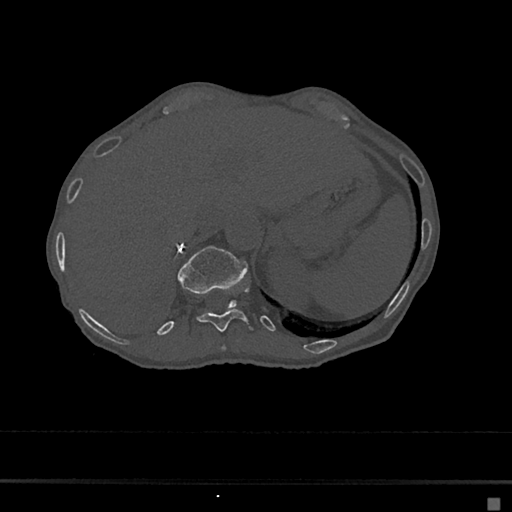
CT including the spine, one axial slice; slice 161 of 797 in the series (ordered by position); bone window (W 1800 / L 400 HU); 0.5 mm slice thickness; 512 × 512 image matrix. Patient: female, 68 years. Case-level facts recorded for this patient, not image findings: primary cancer: renal.
Annotated regions visible in this slice (semi-automatic segmentation, software-assisted and operator-edited):
- T10 vertebra: bounding box <221,346,226,352> (left, top, right, bottom; pixels)
- T11 vertebra: <196,287,254,332>
- T12 vertebra: <177,246,248,308>